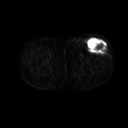
FDG PET of an extremity soft-tissue mass (from a PET/CT study), one axial slice. Slice 234 of 267 in the series (ordered by position). 3.27 mm slice thickness. 128 × 128 image matrix. Male patient, age 64 years. From the clinical record (not read from this slice): histological type: extraskeletal osteosarcoma; grade: high; site of the primary tumour: thigh.
Annotated regions visible in this slice (expert contour drawn on MRI and transferred to this co-registered scan by the dataset authors):
- gross tumour volume (mass): bounding box <88,39,108,53> (left, top, right, bottom; pixels)